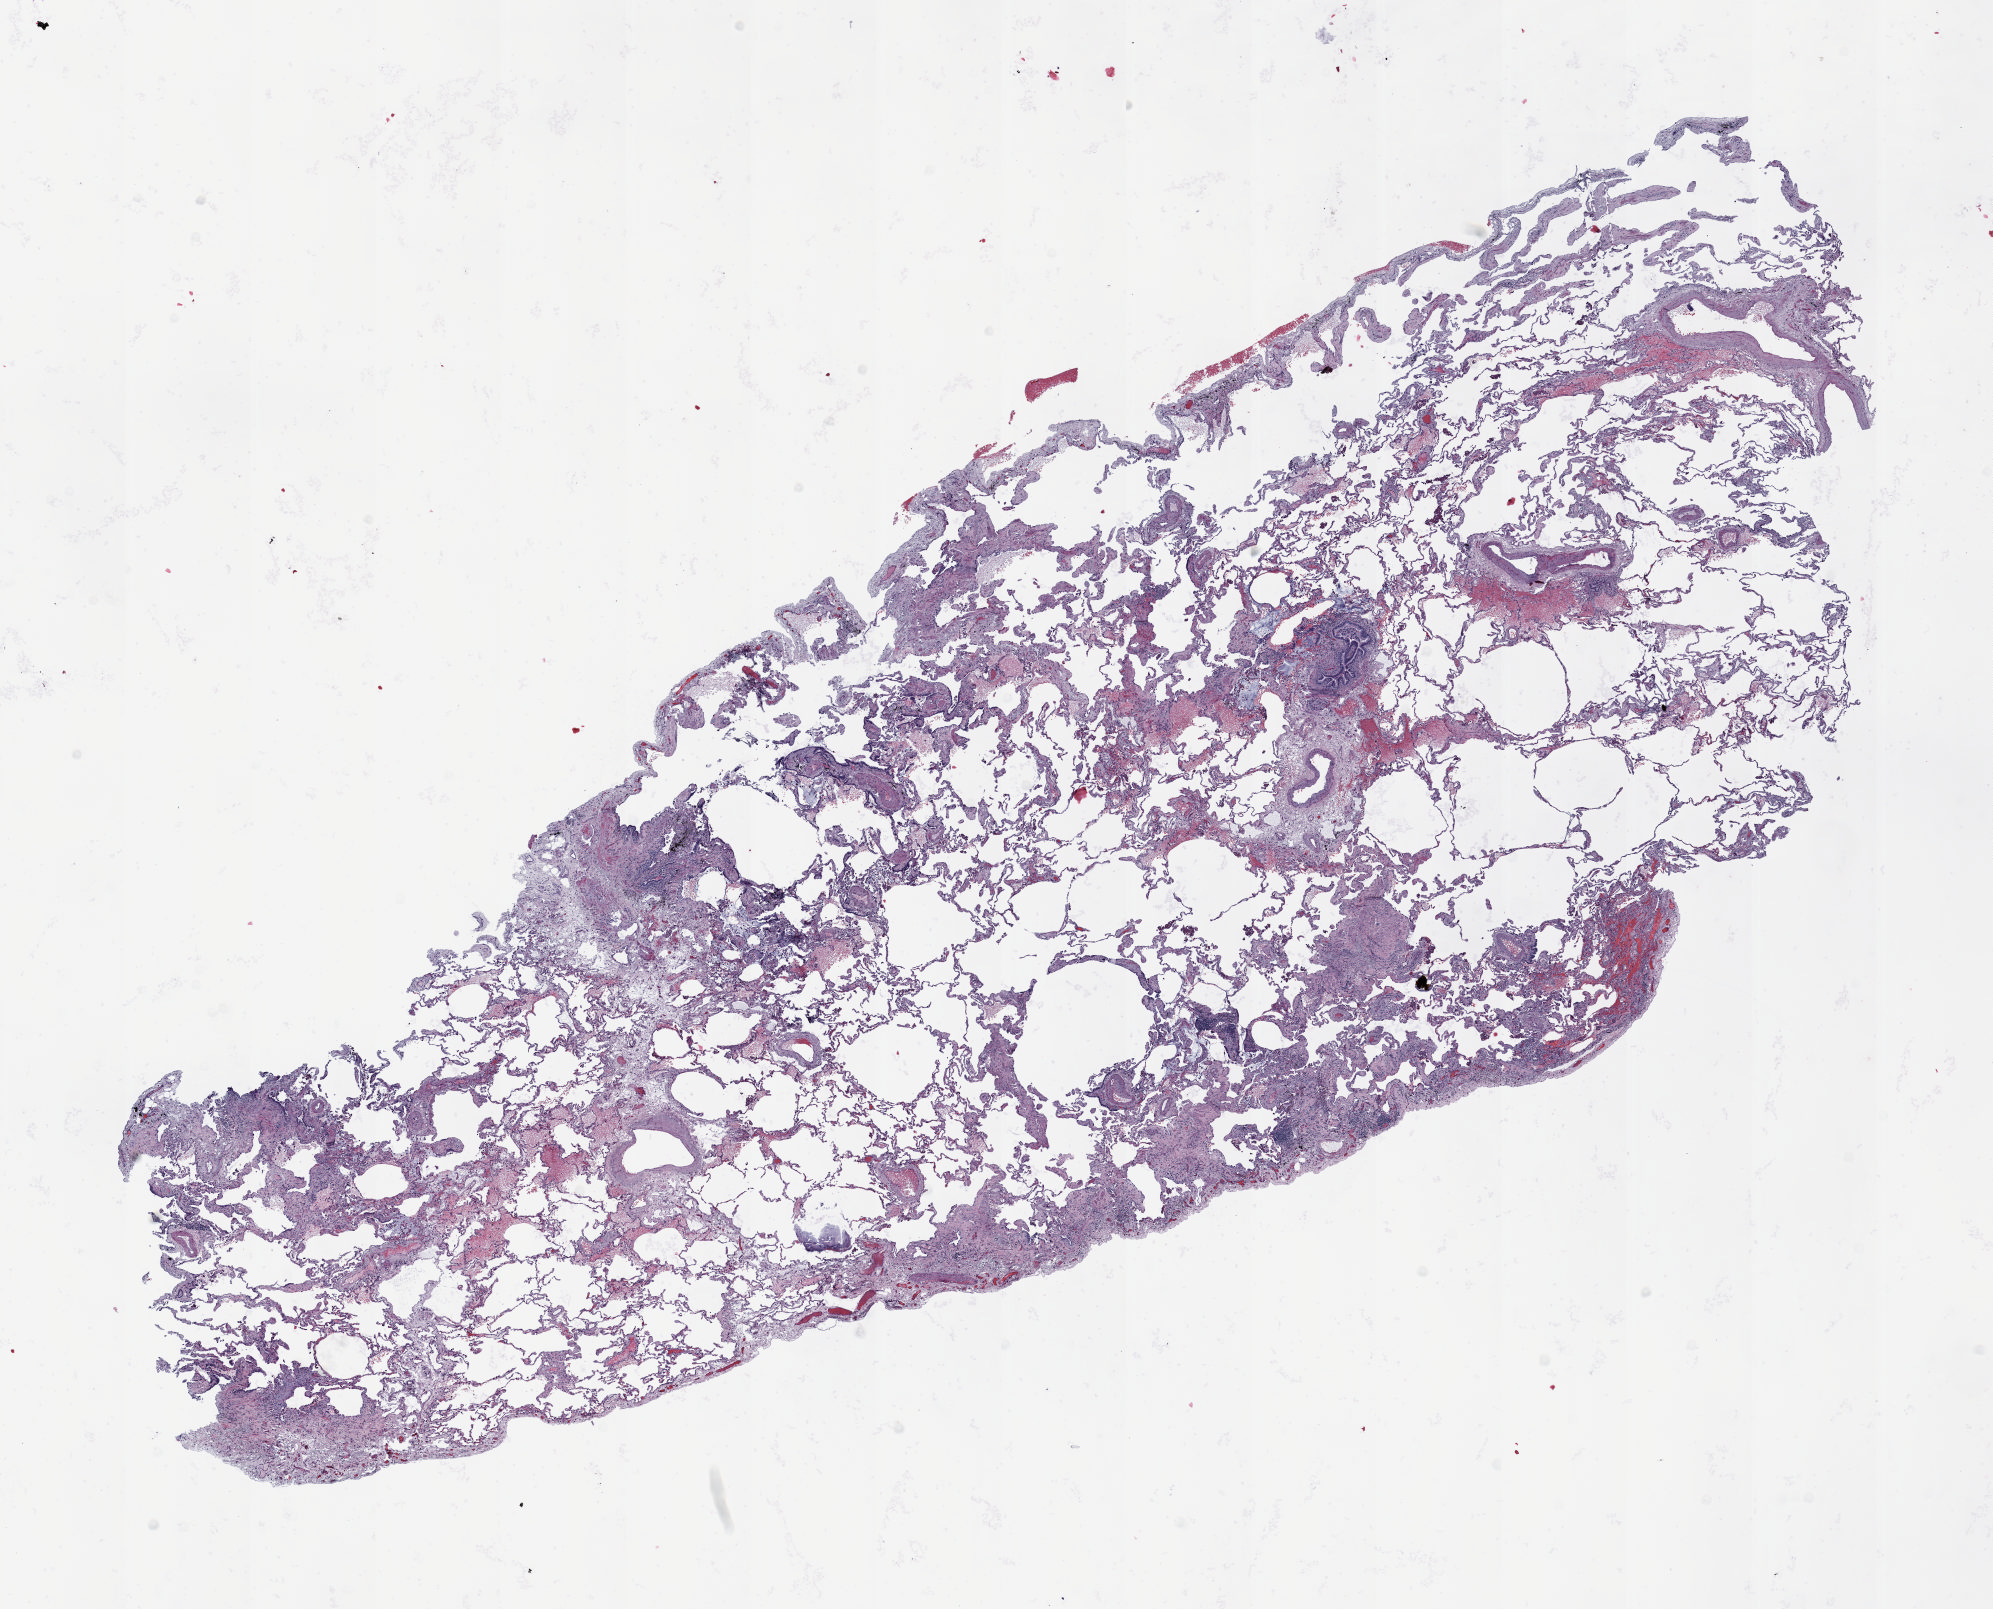
Hematoxylin and eosin (H&E) stained whole-slide image — low-resolution overview of the scanned area, about 16.0 x 12.9 mm (acquisition: 20x scan). Formalin-fixed paraffin-embedded (FFPE) section. Lung. Female patient, aged 70 at enrolment. Current smoker at enrolment. Grade: well differentiated (G1).
• primary tumour location (clinical record): right lower lobe
• tumour size (pathology): 25 mm
• ICD-O-3 topography: lower lobe of lung (C34.3)
• stage (AJCC 6th edition): IA
• participant's lung-cancer diagnosis: Squamous cell carcinoma, NOS